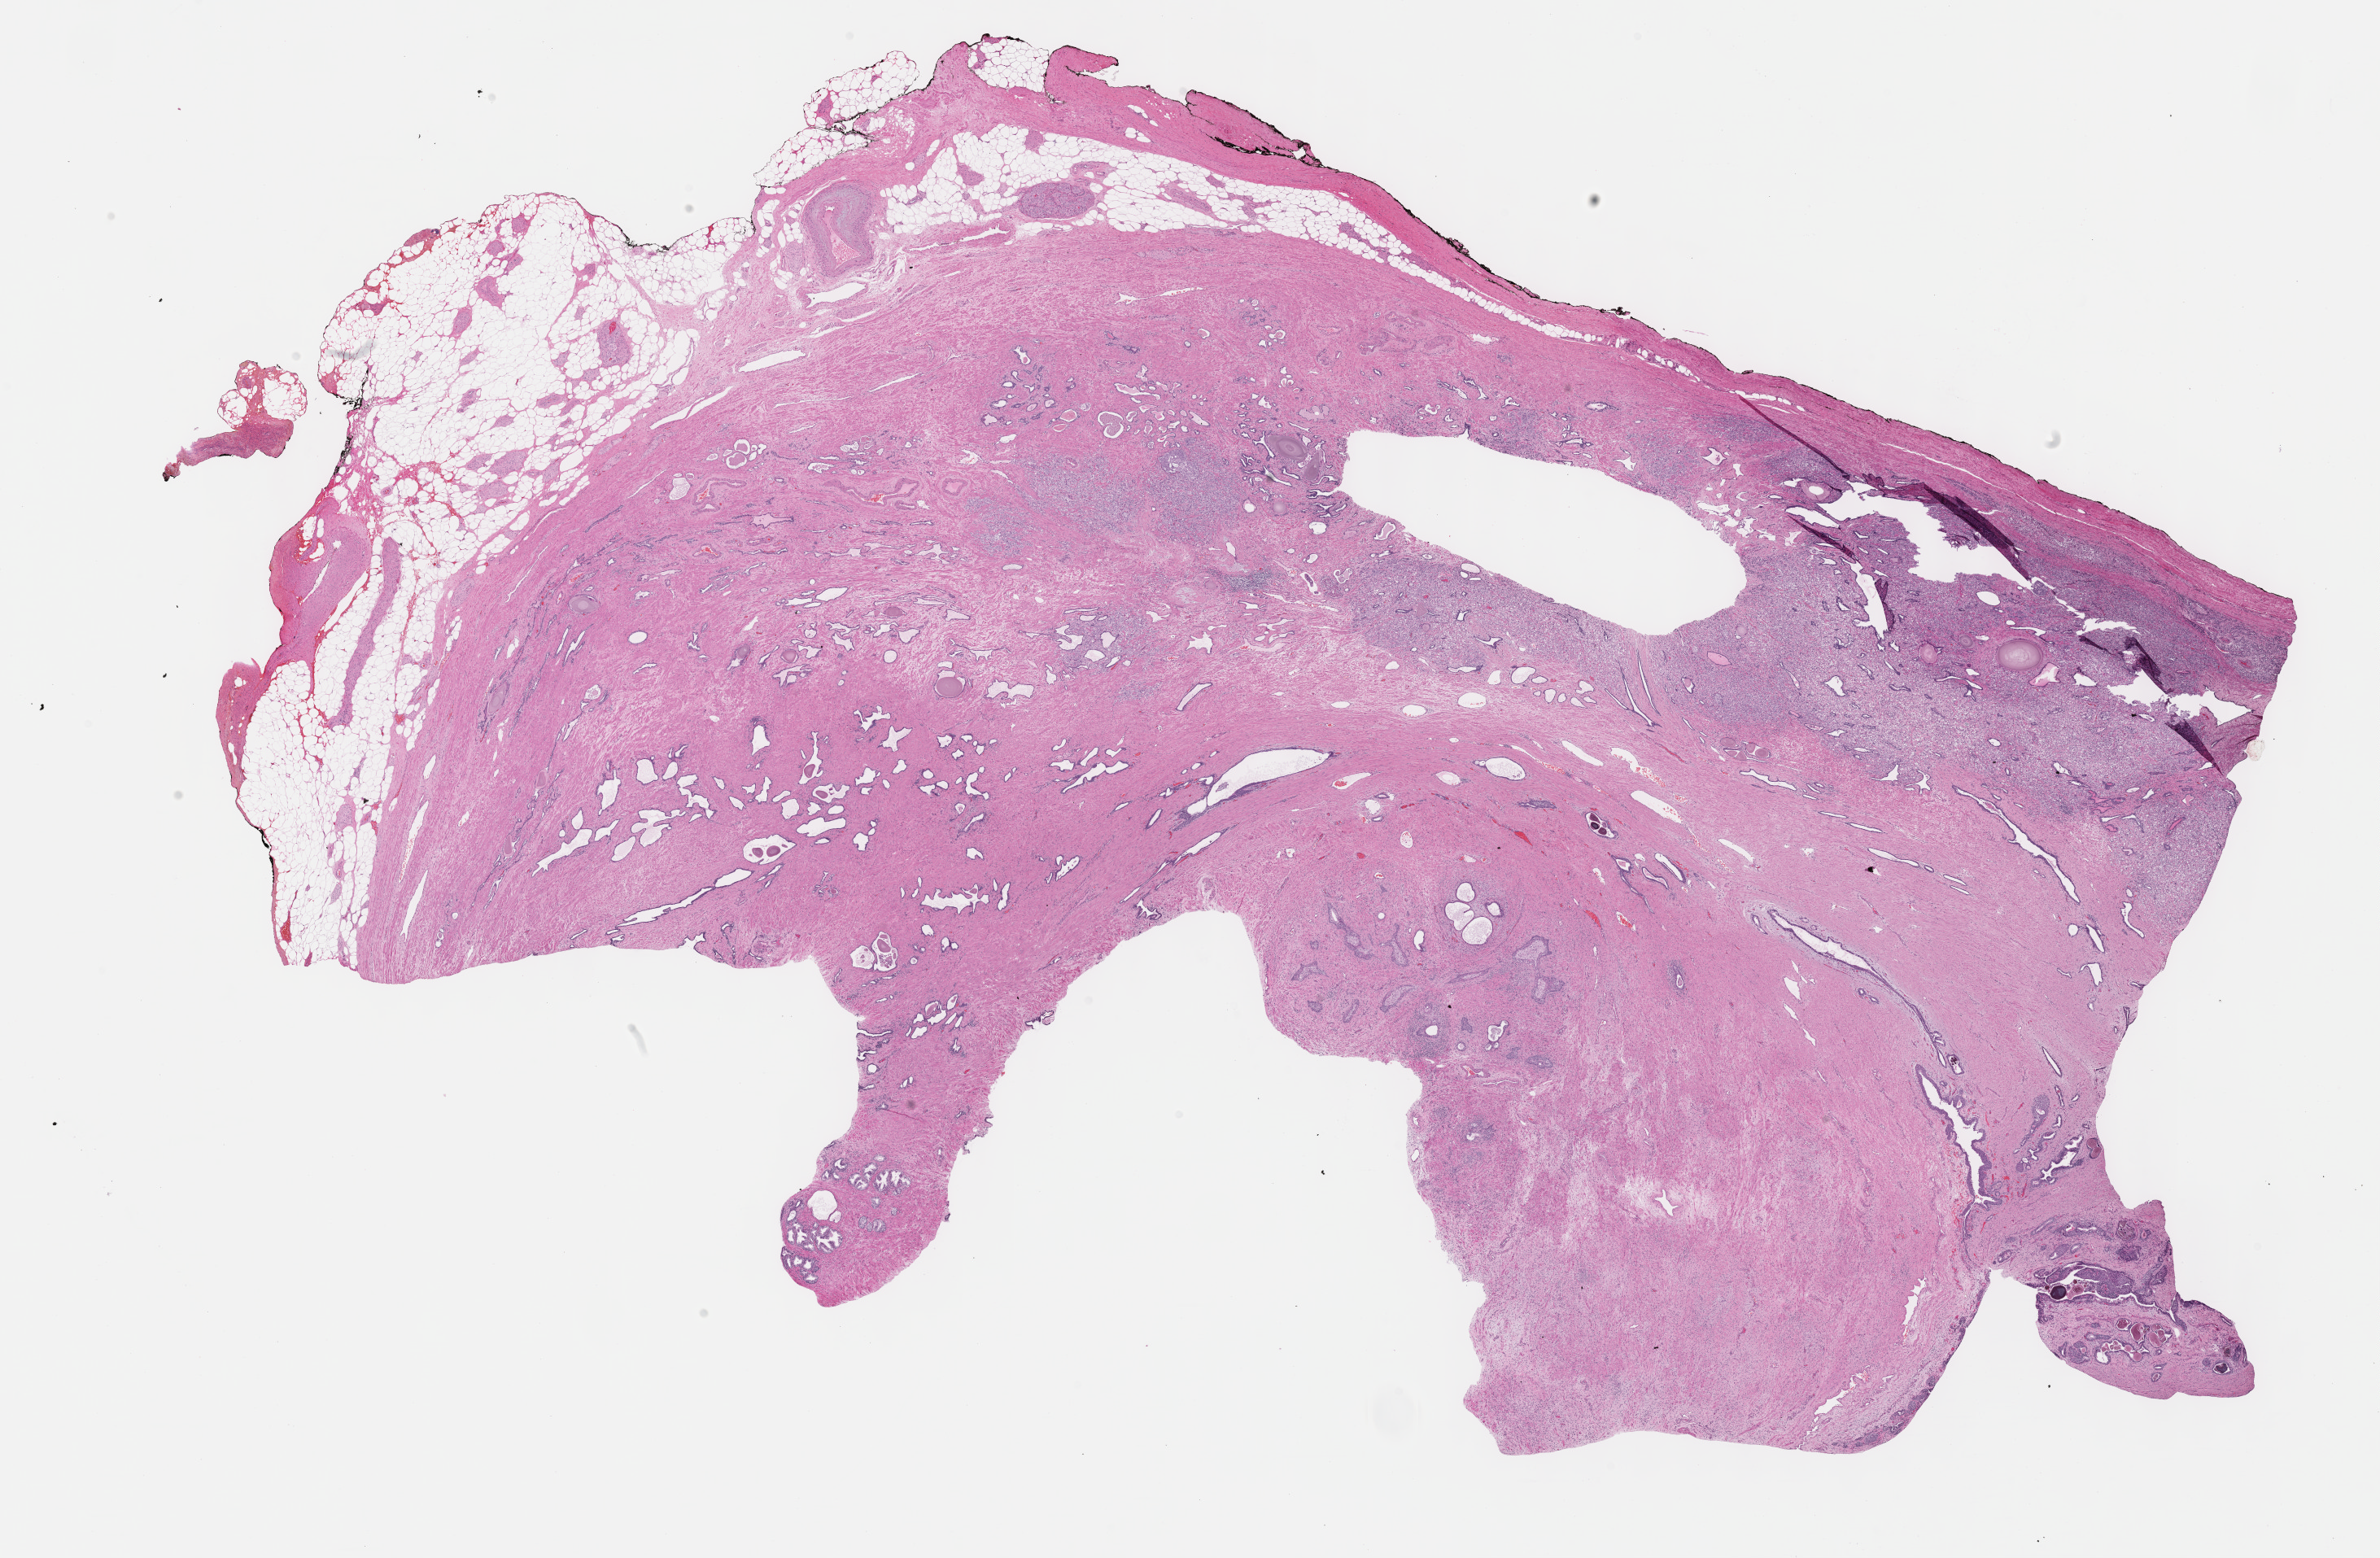
Digitized H&E tissue section (whole slide), shown as a low-resolution overview of the whole scanned area (about 23.7 x 15.5 mm), FFPE section, primary tumour sample from the prostate. Male patient; age at initial diagnosis 62 years. Gleason score: 9 (5+4).
- histologic diagnosis: Adenocarcinoma, NOS (prostate gland)